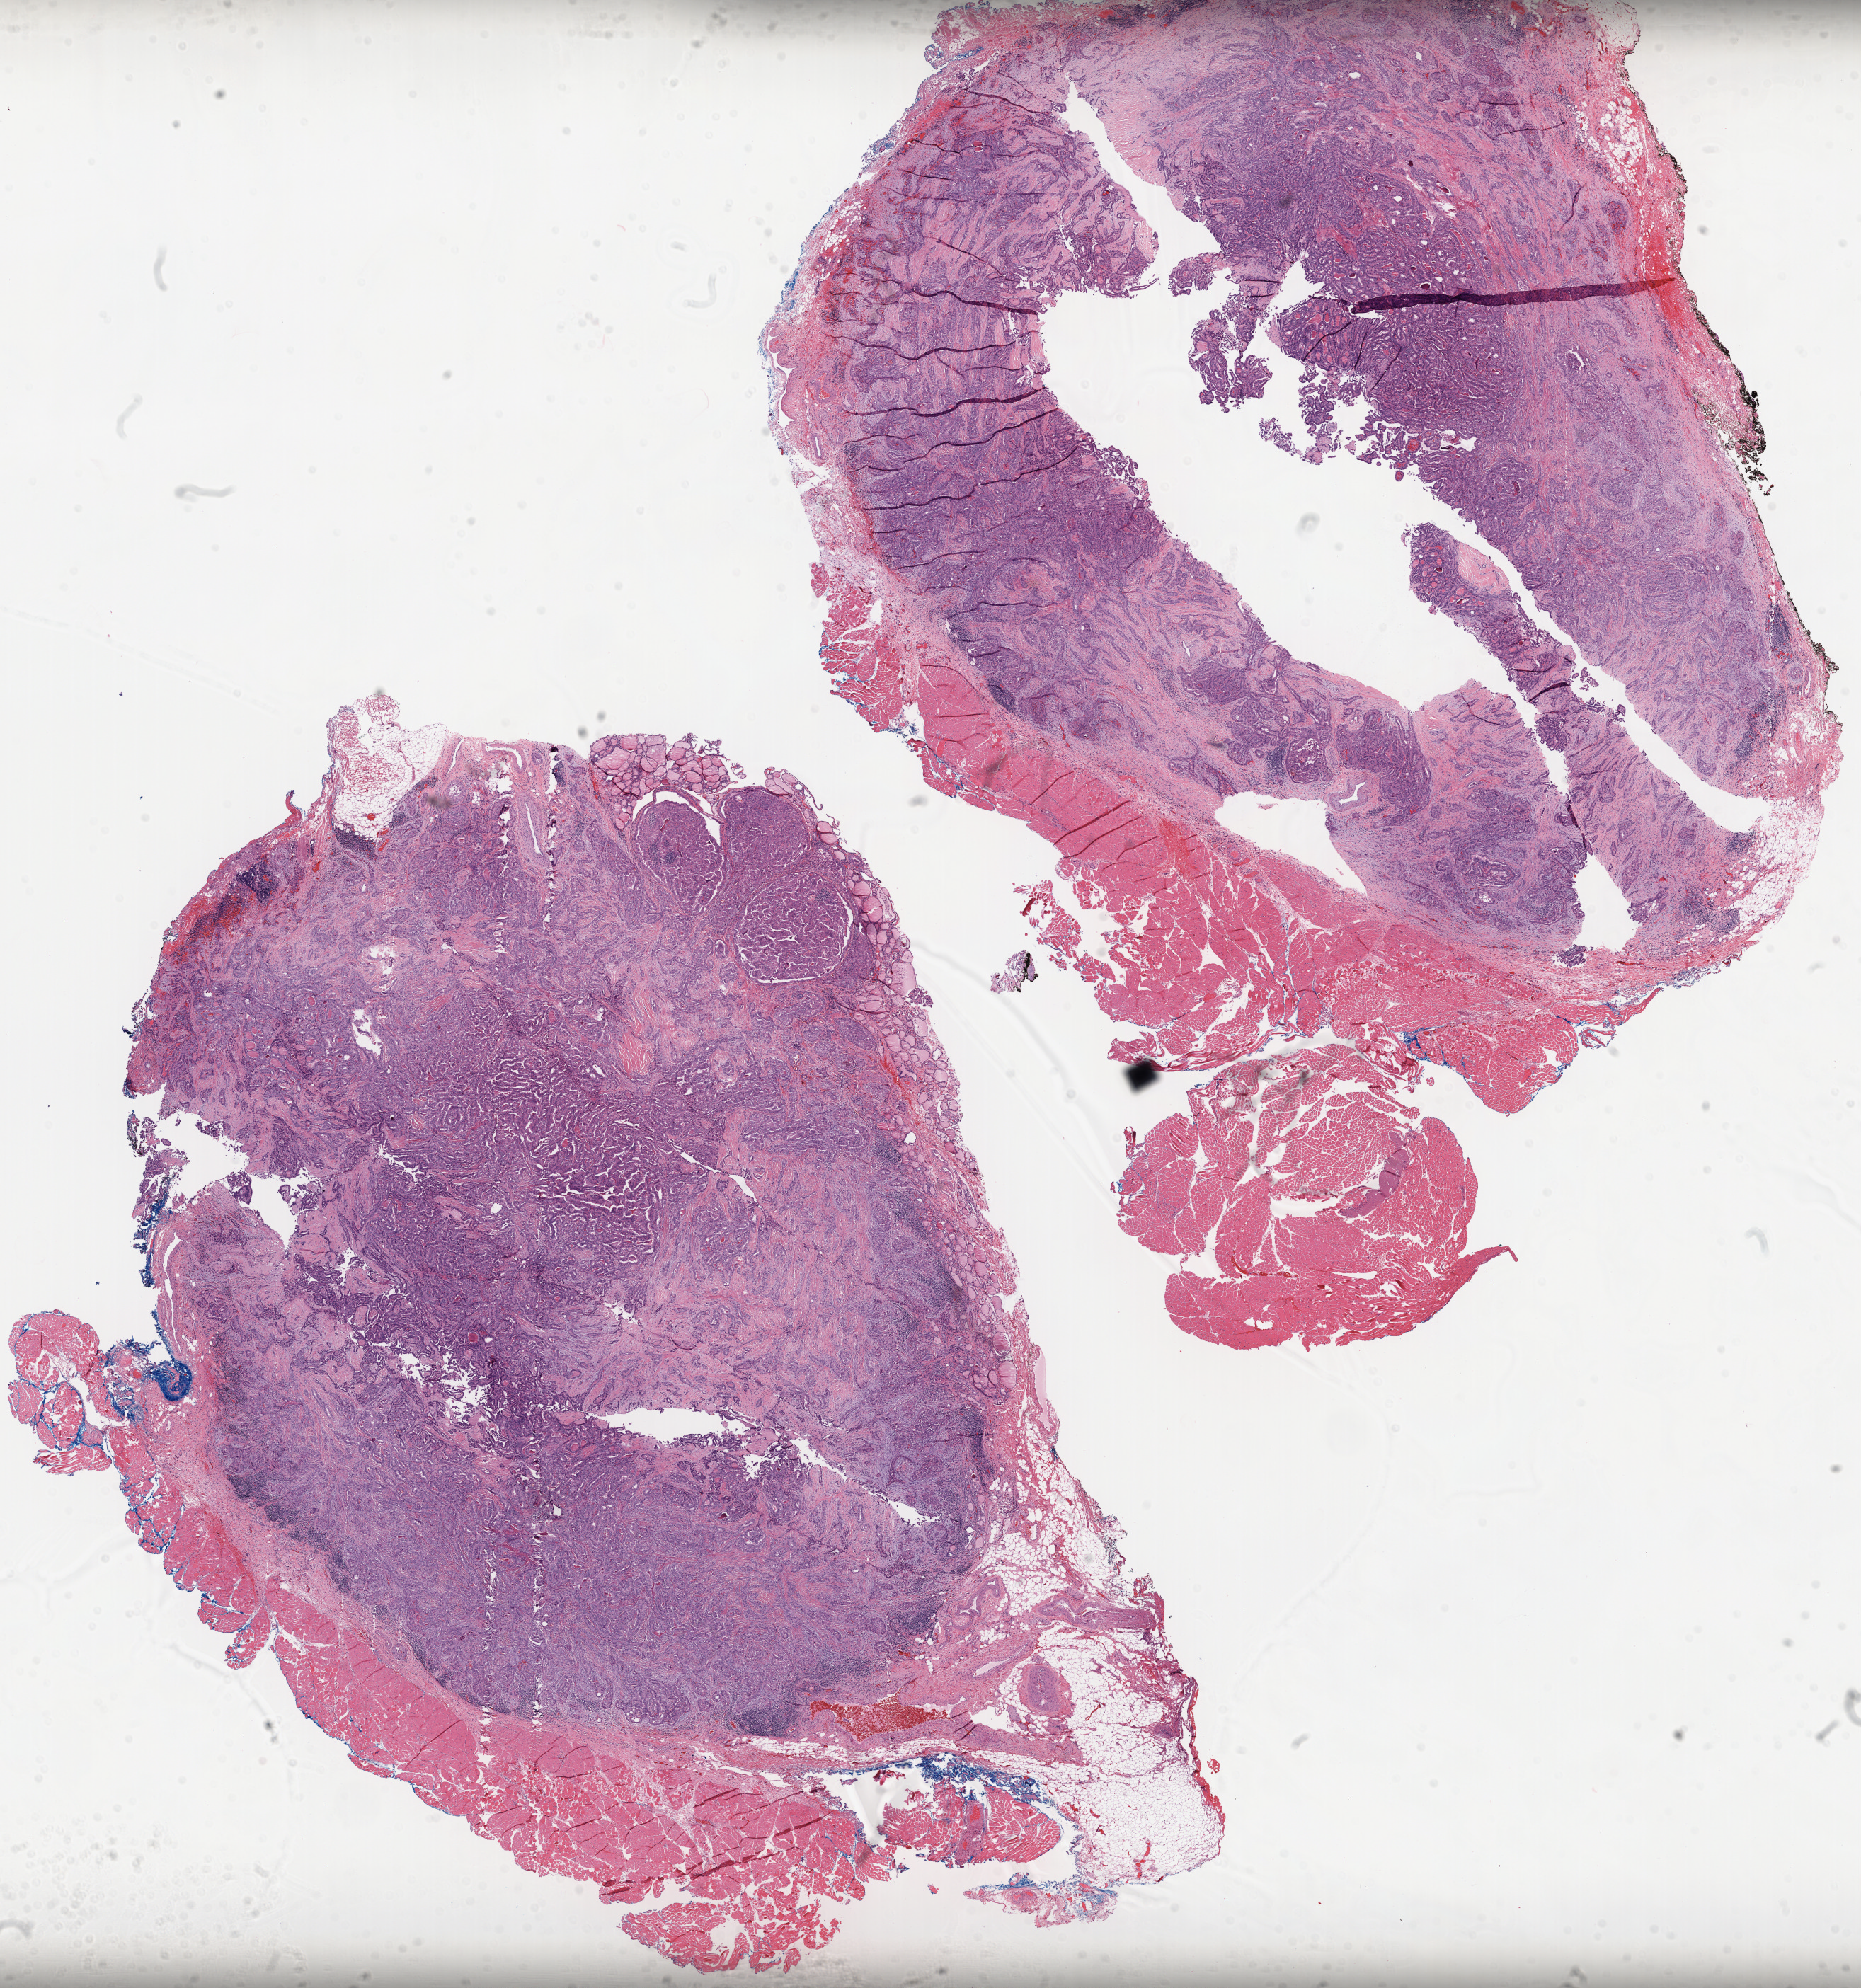
Digitized H&E-stained tissue section (whole slide), low-resolution overview of the scanned area, about 21.2 x 22.7 mm (acquisition: 40x scan); formalin-fixed paraffin-embedded (FFPE) diagnostic section; thyroid, primary tumour sample. Patient: female, age at initial diagnosis 62 years.
Histologic diagnosis: Papillary adenocarcinoma, NOS. AJCC pathologic stage: III (7th edition).